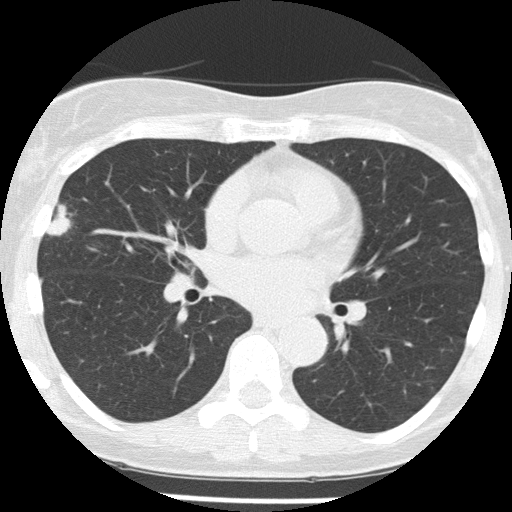
Low-dose screening chest CT, one axial slice; slice 83 of 156 in the series (ordered by position); reconstruction kernel FC51; lung window (W 1500 / L -600 HU); 2 mm slice thickness; 512 × 512 image matrix, field of view 280 × 280 mm.
Outlined on this slice (expert manual segmentation):
- lesion 1 (tumor, middle lobe of right lung): bounding box <47,204,70,236> (left, top, right, bottom; pixels)